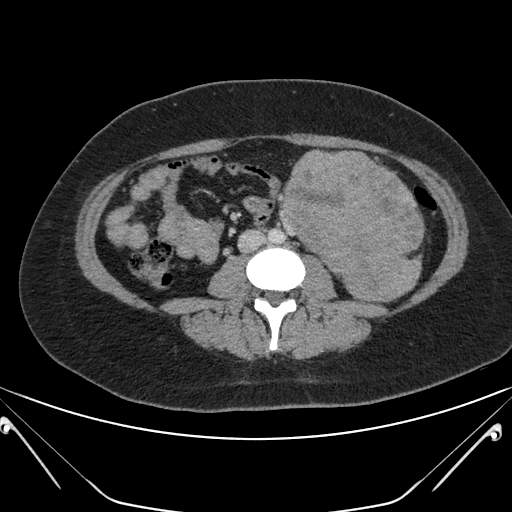
Contrast-enhanced abdominal CT, one axial slice. Slice 87 of 168 in the series (ordered by position). Intravenous contrast given. Soft-tissue window (W 400 / L 40 HU). 3 mm slice thickness. 512 × 512 image matrix, field of view 394 × 394 mm. Female patient, age 26 years. Case-level facts recorded for this patient, not image findings: diagnosis: adrenocortical carcinoma; tumour side: left adrenal; tumour size at pathology: 28 cm; Ki-67 index: 20 %; stage (as recorded): 2.
Annotated regions visible in this slice (semi-automatic segmentation, software-assisted and operator-edited):
- mass: bounding box <286,152,422,300> (left, top, right, bottom; pixels)